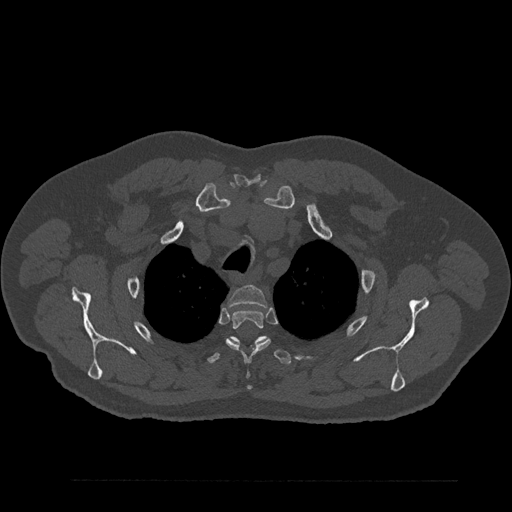
CT including the spine, one axial slice. Slice 680 of 797 in the series (ordered by position). Bone window (W 1800 / L 400 HU). 0.5 mm slice thickness. 512 × 512 image matrix. Patient: male, 61 years. Case-level facts recorded for this patient, not image findings: primary cancer: prostate.
Annotated regions visible in this slice (semi-automatic segmentation, software-assisted and operator-edited):
- T2 vertebra: bounding box <228,285,267,307> (left, top, right, bottom; pixels)
- T3 vertebra: <225,309,271,389>
- T4 vertebra: <207,336,291,365>